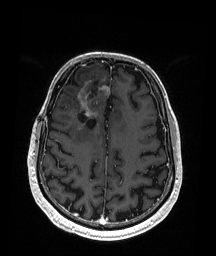
Brain MRI from a brain-tumour surgery series, one axial slice; slice 64 of 192 in the series (ordered by position); T1-weighted post-contrast; 1 mm slice thickness; 216 × 256 image matrix, field of view 211 × 250 mm. From the clinical record (not read from this slice): histopathology: Astrocytoma; WHO grade: 3; IDH mutation: yes.
Annotated regions visible in this slice (expert manual segmentation):
- previous resection cavity: bounding box (x1, y1, x2, y2) in pixels: (79, 81, 100, 124)
- tumour: (73, 81, 109, 135)